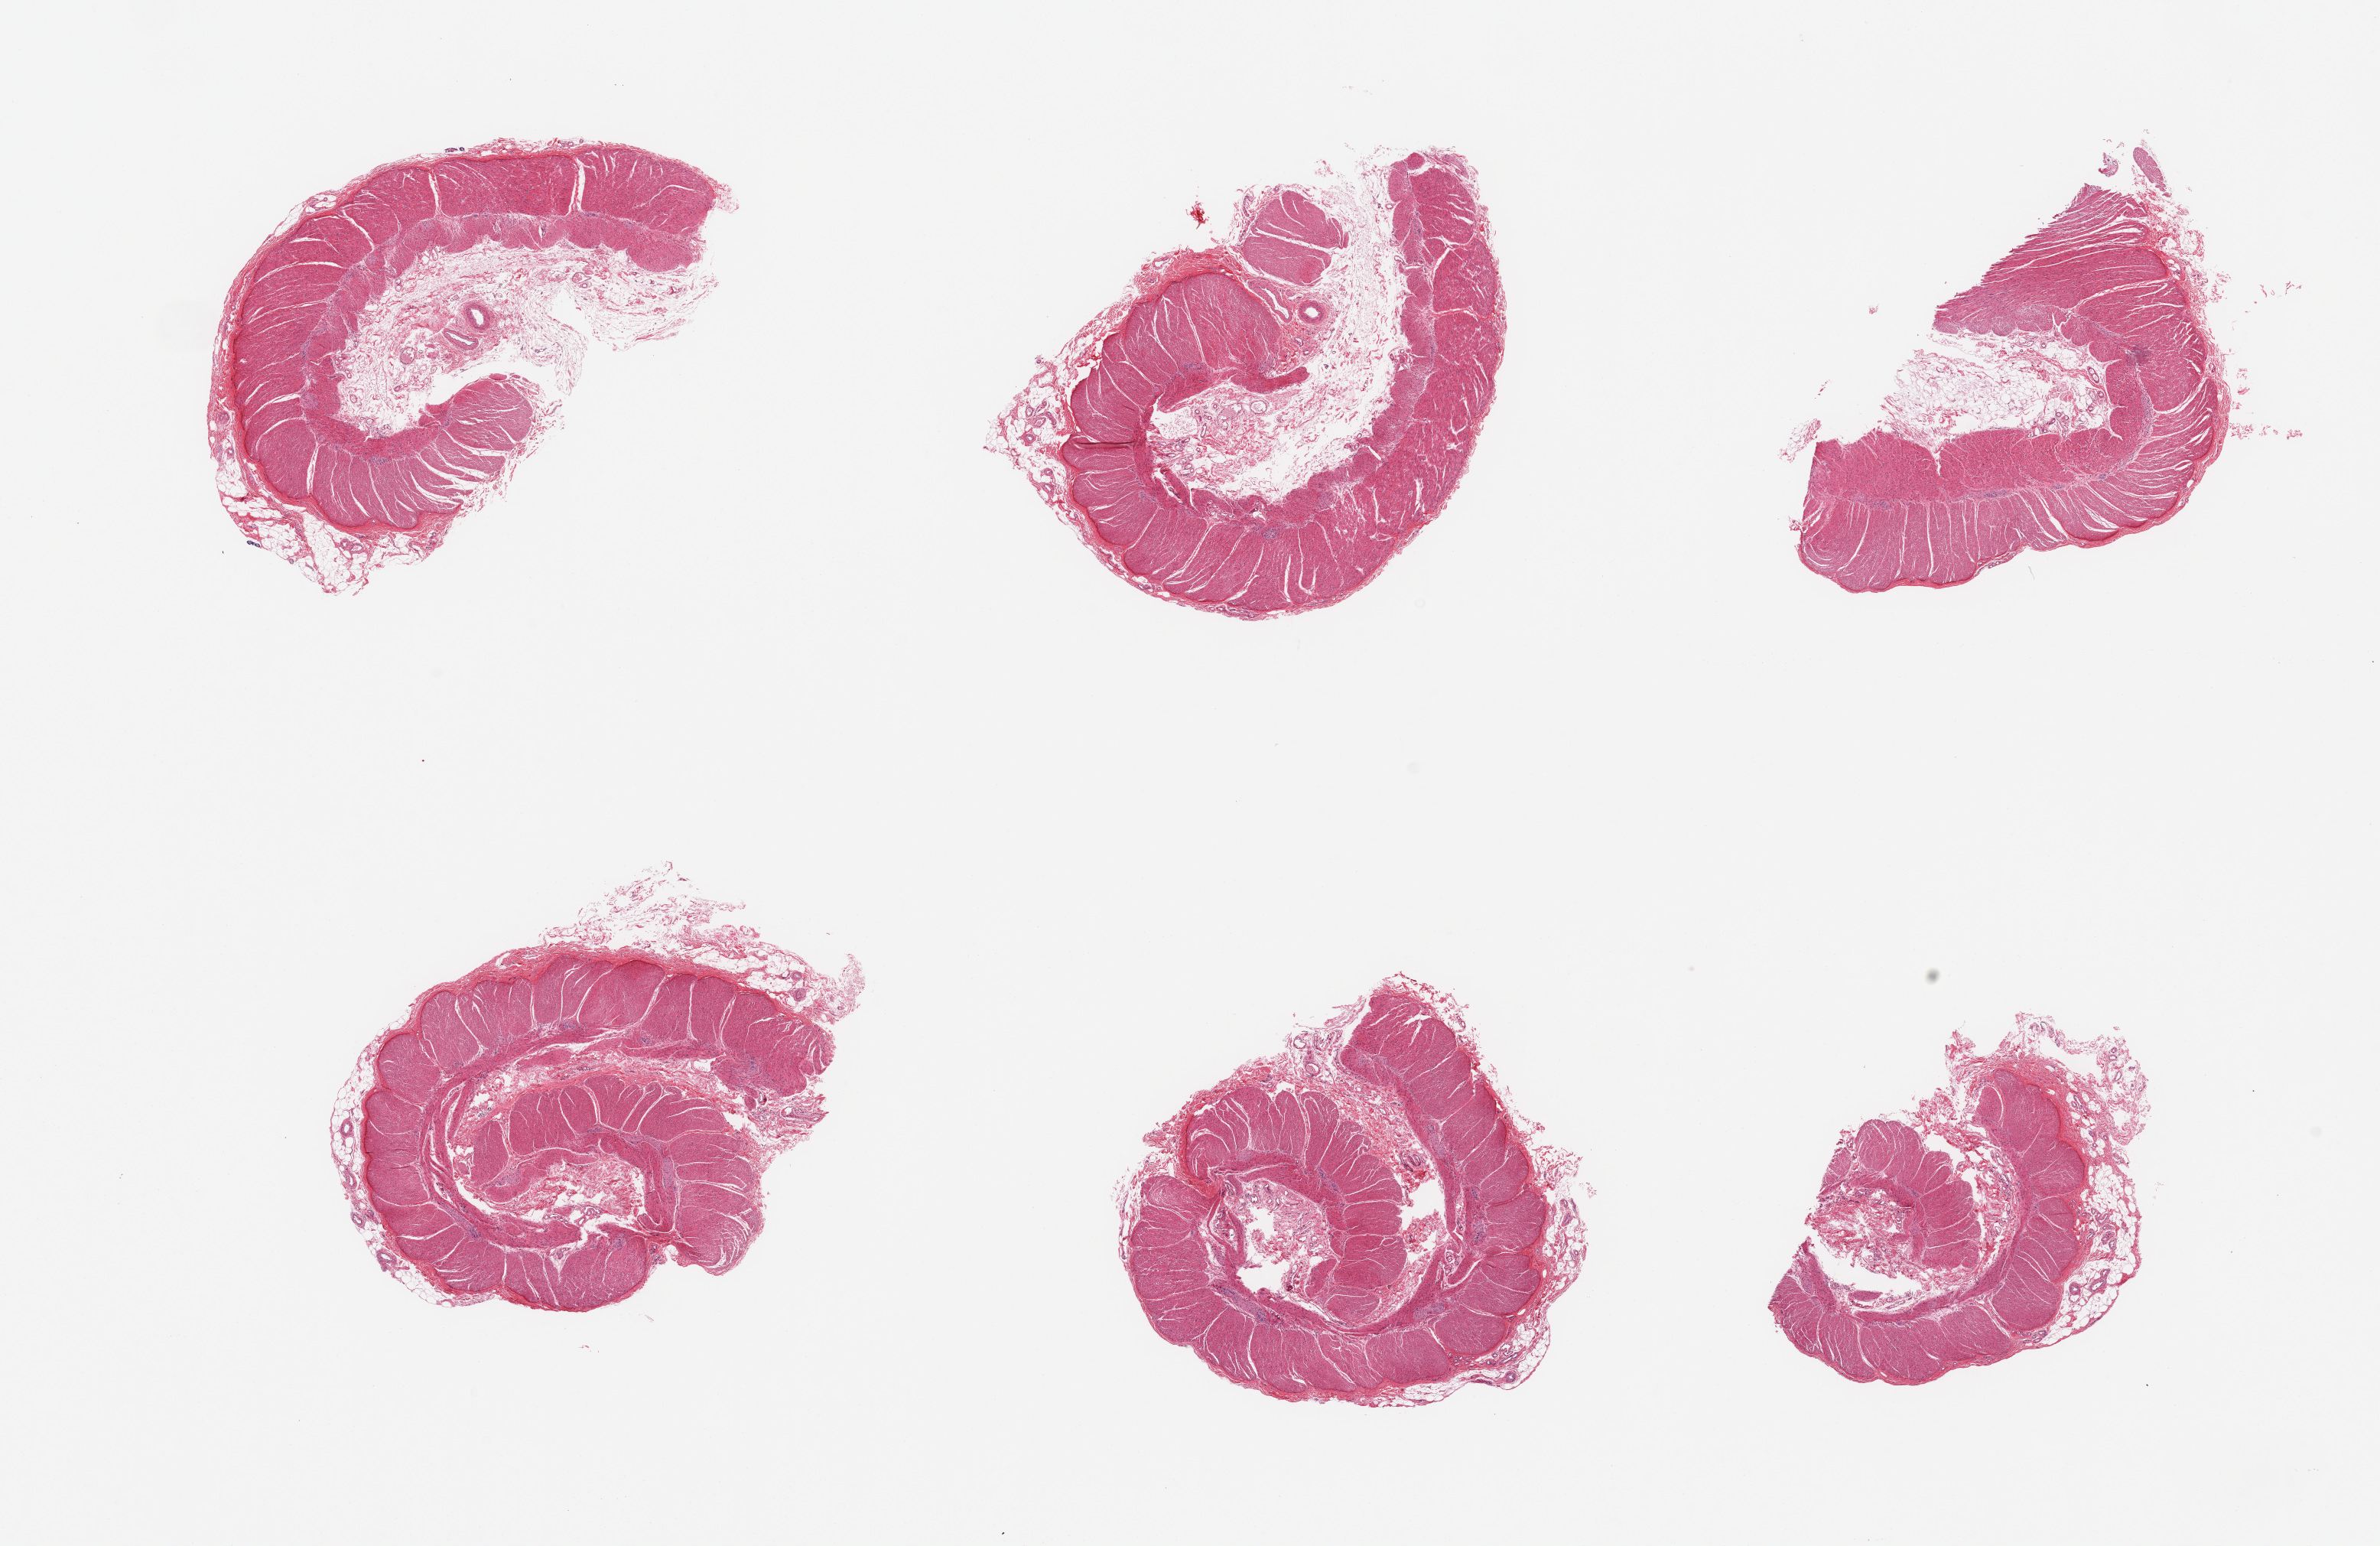
Digitized haematoxylin and eosin-stained section, brightfield — a low-resolution overview of the entire scanned area, about 24.6 x 16.0 mm, PAXgene-fixed, paraffin-embedded tissue, sampled site (target tissue): transverse colon, donor tissue sample. Female donor.
Pathologist's review note for this sample: 6 pieces; no mucosa, only muscularis propria.